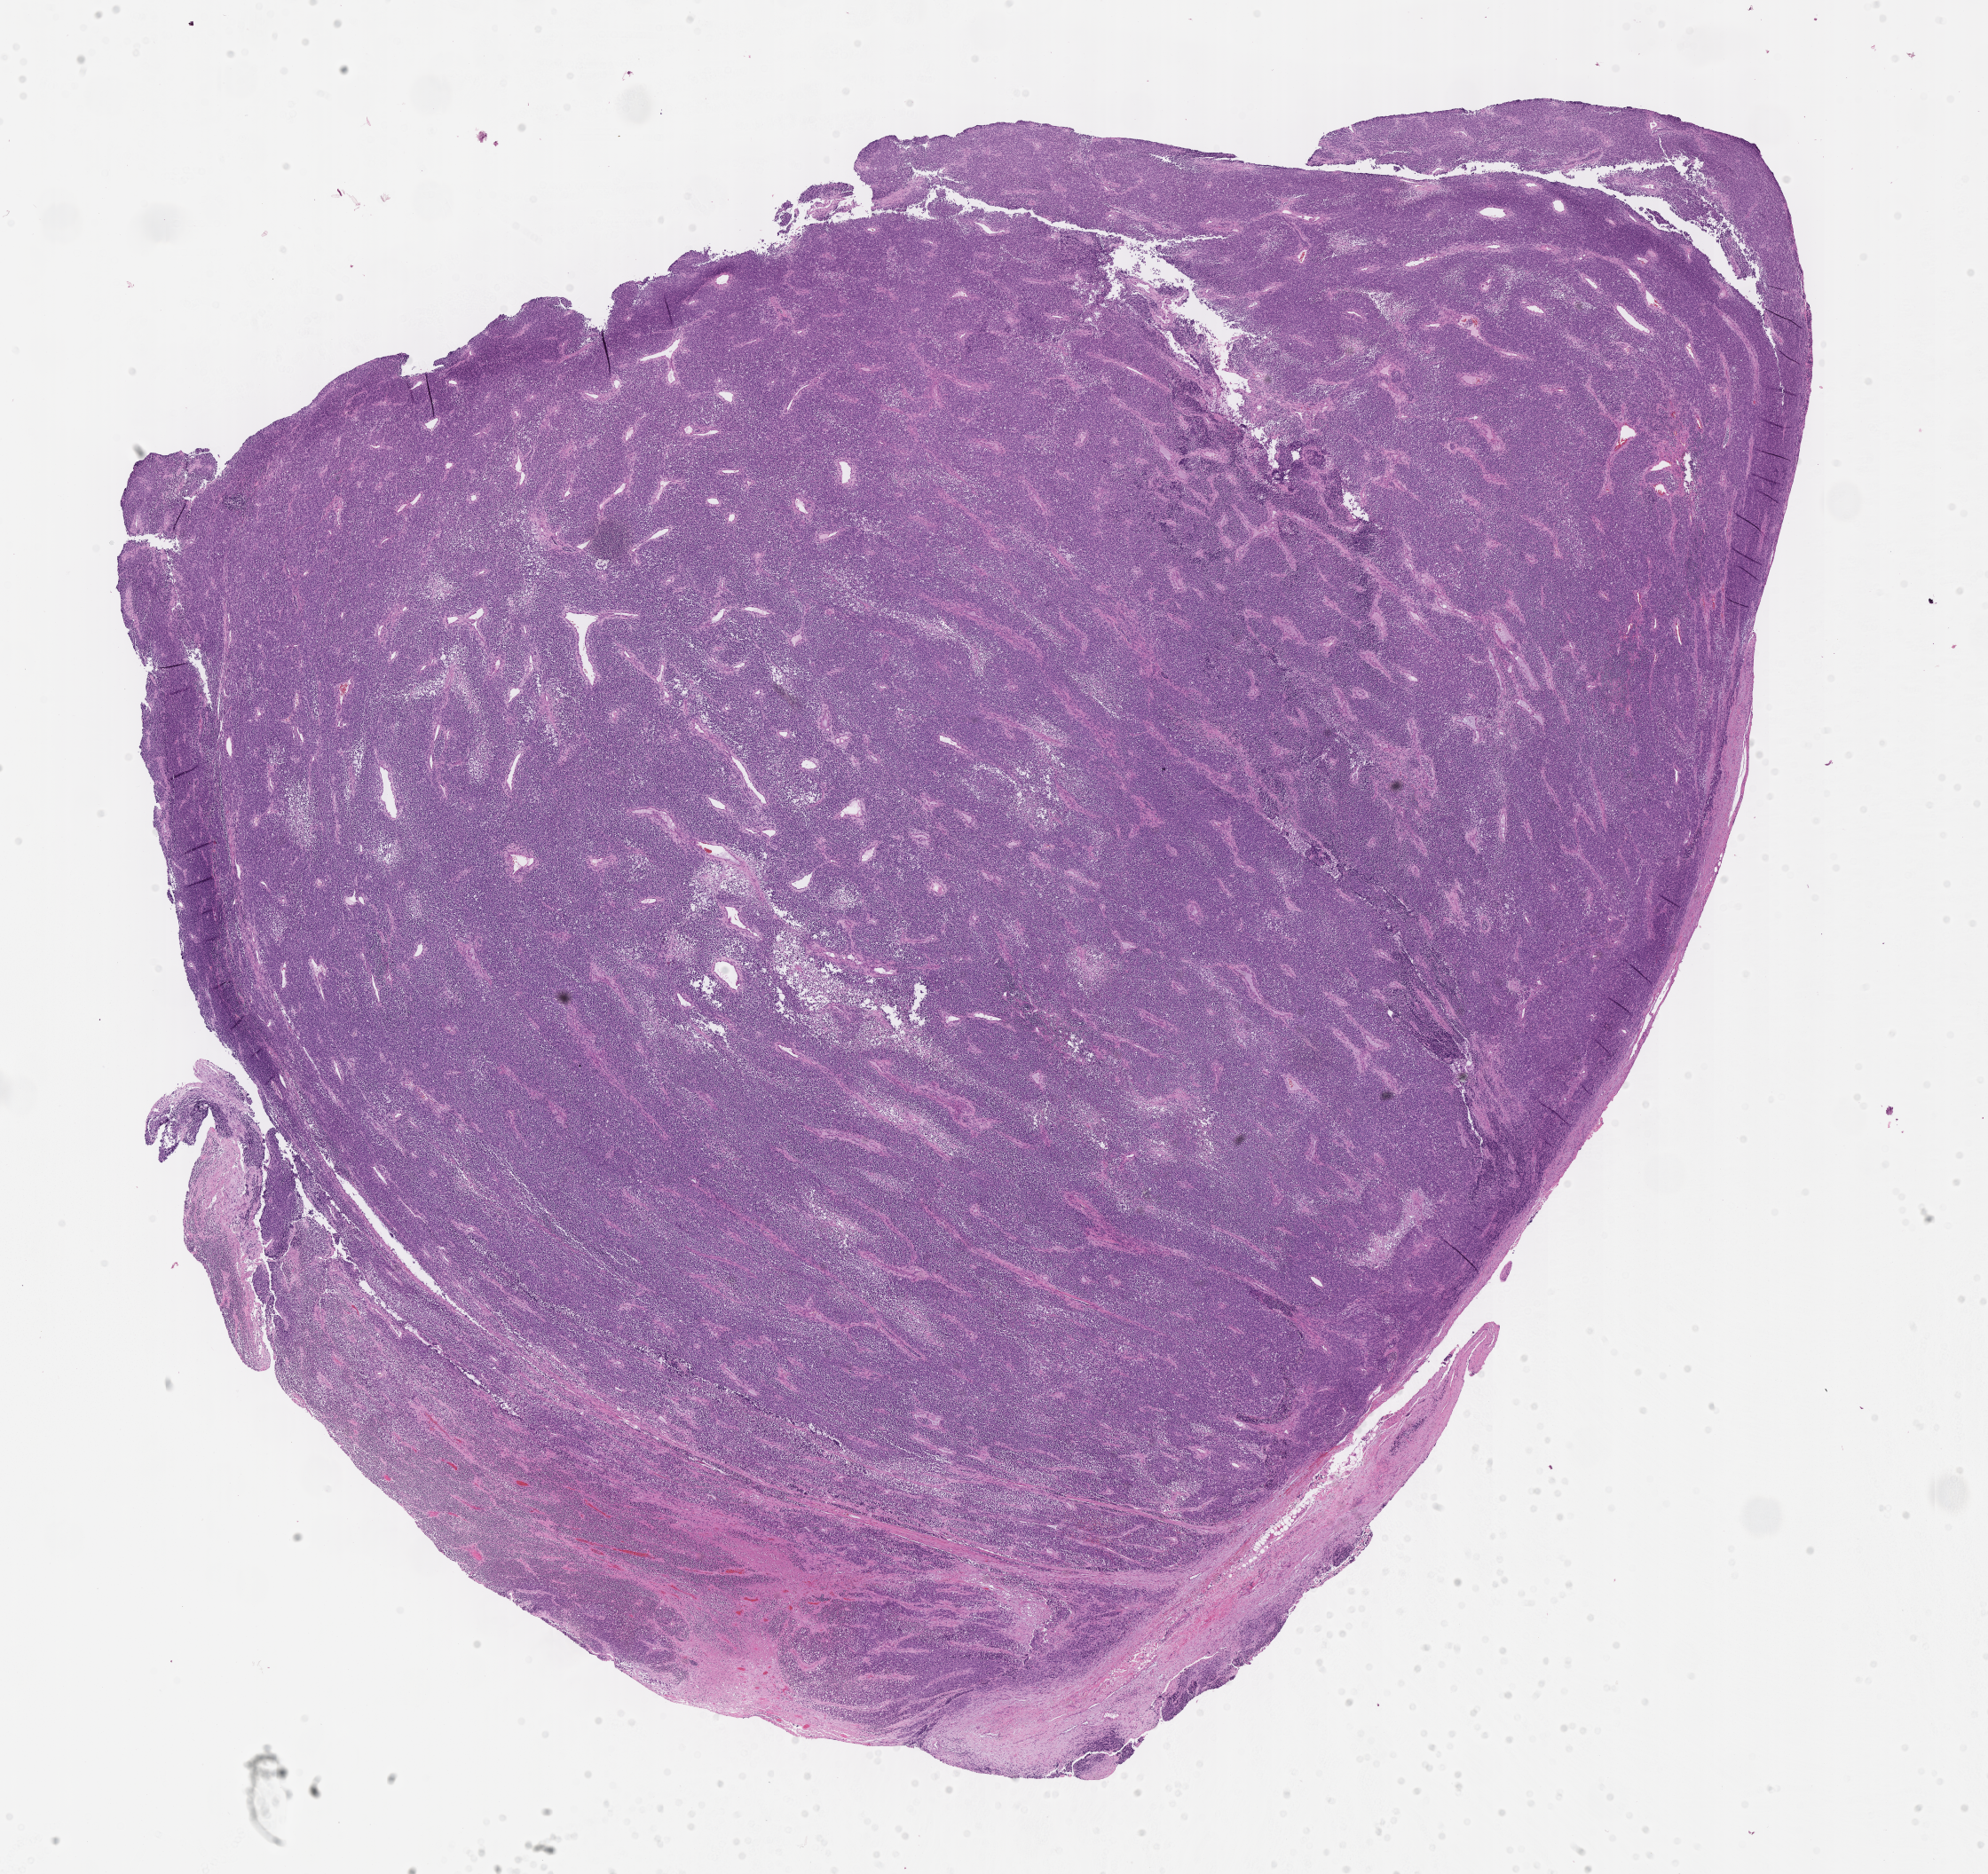
Haematoxylin and eosin whole-slide image of tumor tissue — a low-resolution overview of the entire scanned area, about 18.1 x 17.1 mm, formalin-fixed paraffin-embedded section, sample anatomic site: lymph node. Male patient, age at diagnosis 7.0 years.
* stage (as recorded): 3
* primary site (case record): parapharyngeal Area
* diagnosis: rhabdomyosarcoma; histological classification: embryonal rhabdomyosarcoma
* metastatic status at presentation (as recorded): non-metastatic